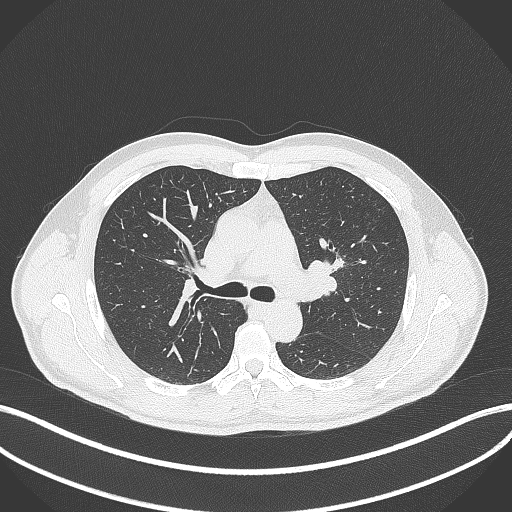
Chest CT, one axial slice. Position 272 of 392 along the scan axis. Reconstruction kernel B70f. 120 kVp. Lung window (W 1500 / L -600 HU). 1 mm slice thickness. 512 × 512 image matrix, field of view 400 × 400 mm. Male patient, age 50 years. Case-level facts recorded for this patient, not image findings: clinical TNM (as recorded): T1c N1 M1b.
Structures marked on this image (rectangle marked by the reading radiologist):
- lung tumour (recorded histology: squamous cell carcinoma): box from (x=334, y=251) to (x=344, y=274) px